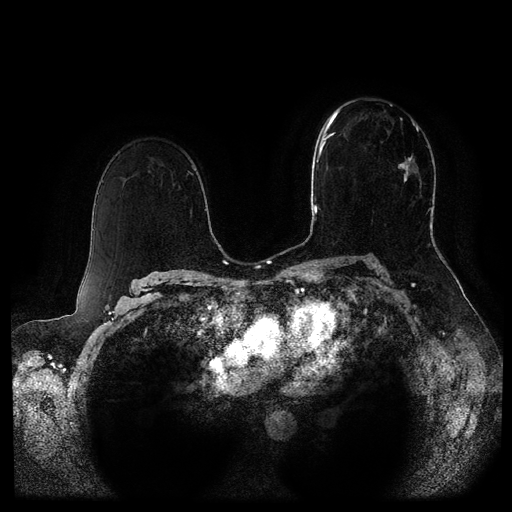
Breast MRI (dynamic contrast-enhanced, multi-phase), one axial slice; position 61 of 116 along the scan axis; dynamic contrast-enhanced series, time point 2 of 5 at this slice position (early post-contrast); 1.5 T; TE 2.6 ms, TR 5.3 ms; 512 × 512 image matrix. Patient: female, 51 years.
Structures marked on this image (semi-automatically segmented with operator editing):
- breast lesion (labelled 'tumour' in the annotation; benign lesions carry a separate 'benign' label): bounding box (x1, y1, x2, y2) in pixels: (398, 155, 414, 184)